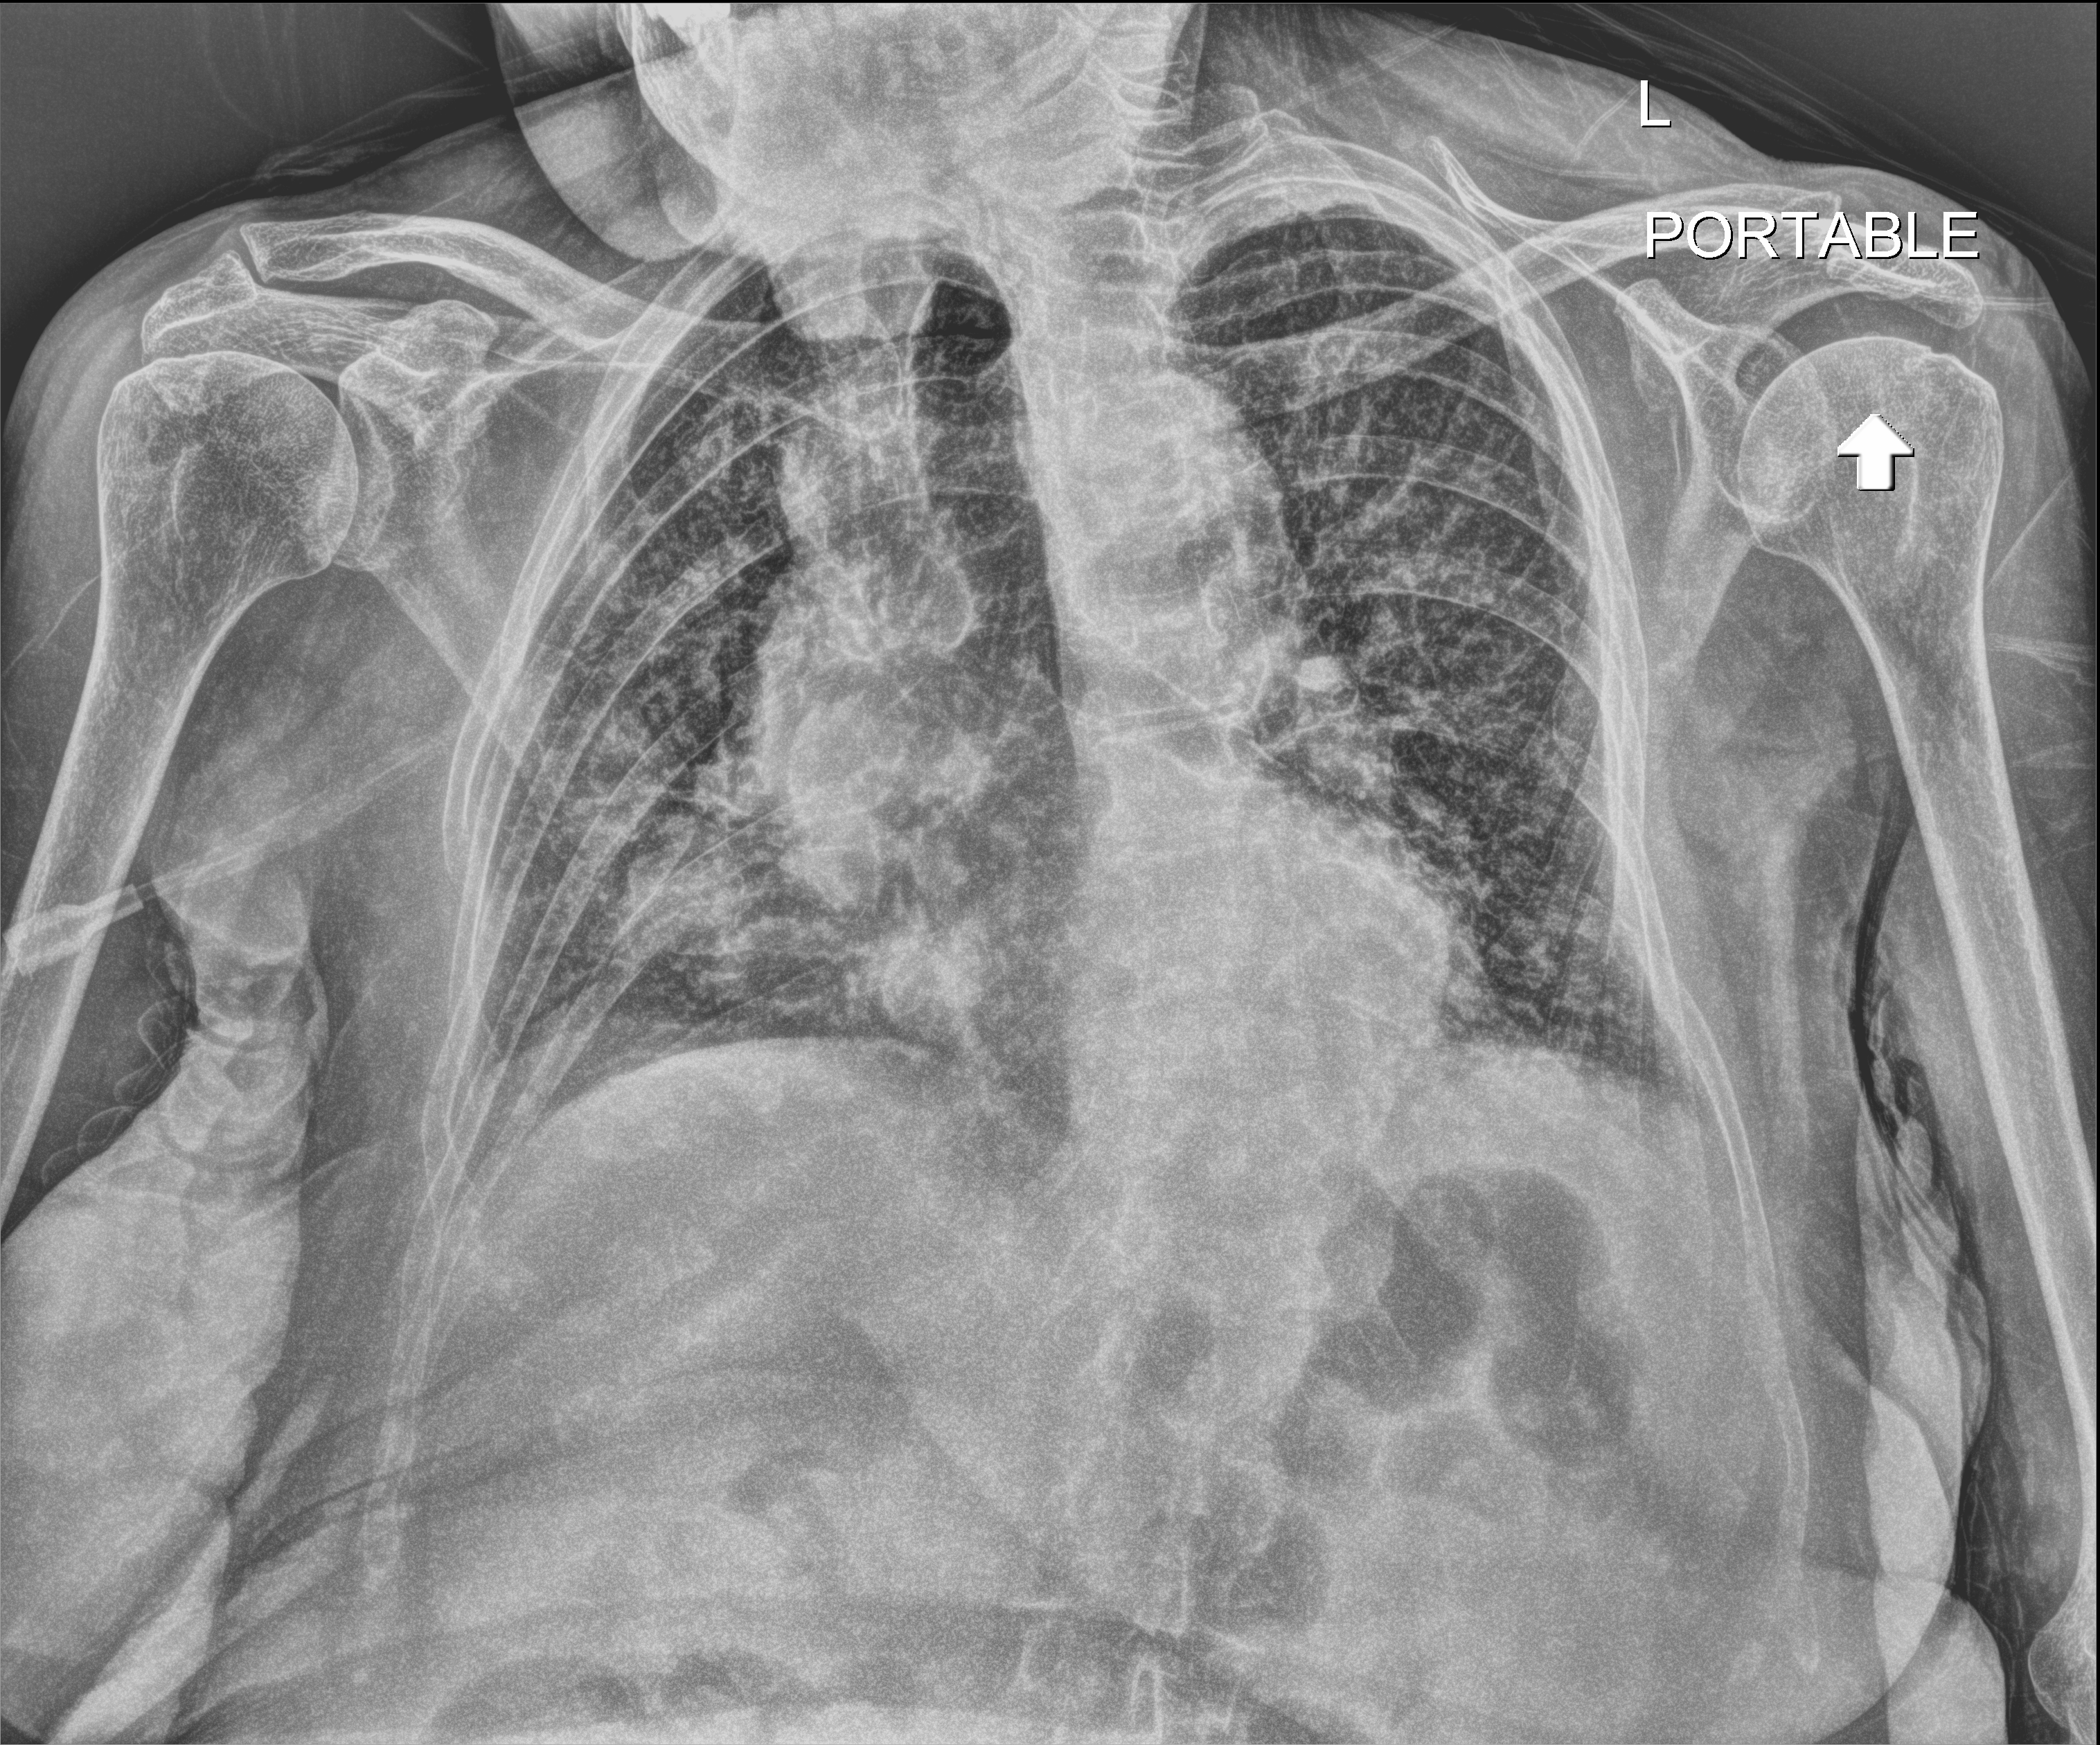
Chest radiograph. Female patient hospitalised with COVID-19, age 75–90 years.
Admission-level facts for this patient (not findings on this image; timing relative to this image not recorded): mechanically ventilated during this hospital stay: no.